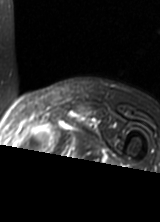
MRI of an extremity soft-tissue mass, one axial slice. Position 53 of 69 along the scan axis. T2-weighted fat-saturated. MR volume resampled by the dataset authors to the PET/CT grid (not the native acquisition matrix). 3.27 mm slice thickness. 160 × 222 image matrix, field of view 156 × 217 mm. Female patient. From the clinical record (not read from this slice): histological type: pleomorphic leiomyosarcoma; grade: high; site of the primary tumour: left thigh.
Structures marked on this image (expert contour drawn on MRI and transferred to this co-registered scan by the dataset authors):
- gross tumour volume including surrounding oedema: bounding box <27,125,74,149> (left, top, right, bottom; pixels)